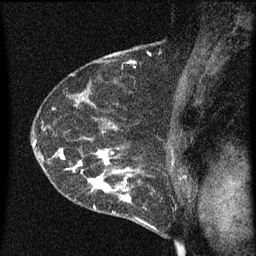
Breast MRI (dynamic contrast-enhanced), one sagittal slice. Slice 45 of 60 in the series (ordered by position). Dynamic contrast-enhanced series, image 2 of 3 at this slice position (ordered by acquisition). 1.5 T. TE 4.2 ms, TR 8 ms. 2 mm slice thickness. 256 × 256 image matrix. Female patient, age 54 years.
Annotated regions visible in this slice (semi-automatically segmented with operator editing):
- analysis volume of interest (the breast-tissue region the enhancement analysis was run in; not a lesion): box from (x=49, y=138) to (x=164, y=209) px
- tumour enhancement mask (voxels above the 70 % enhancement threshold inside the analysis volume of interest): (x=54, y=148)–(x=144, y=209)